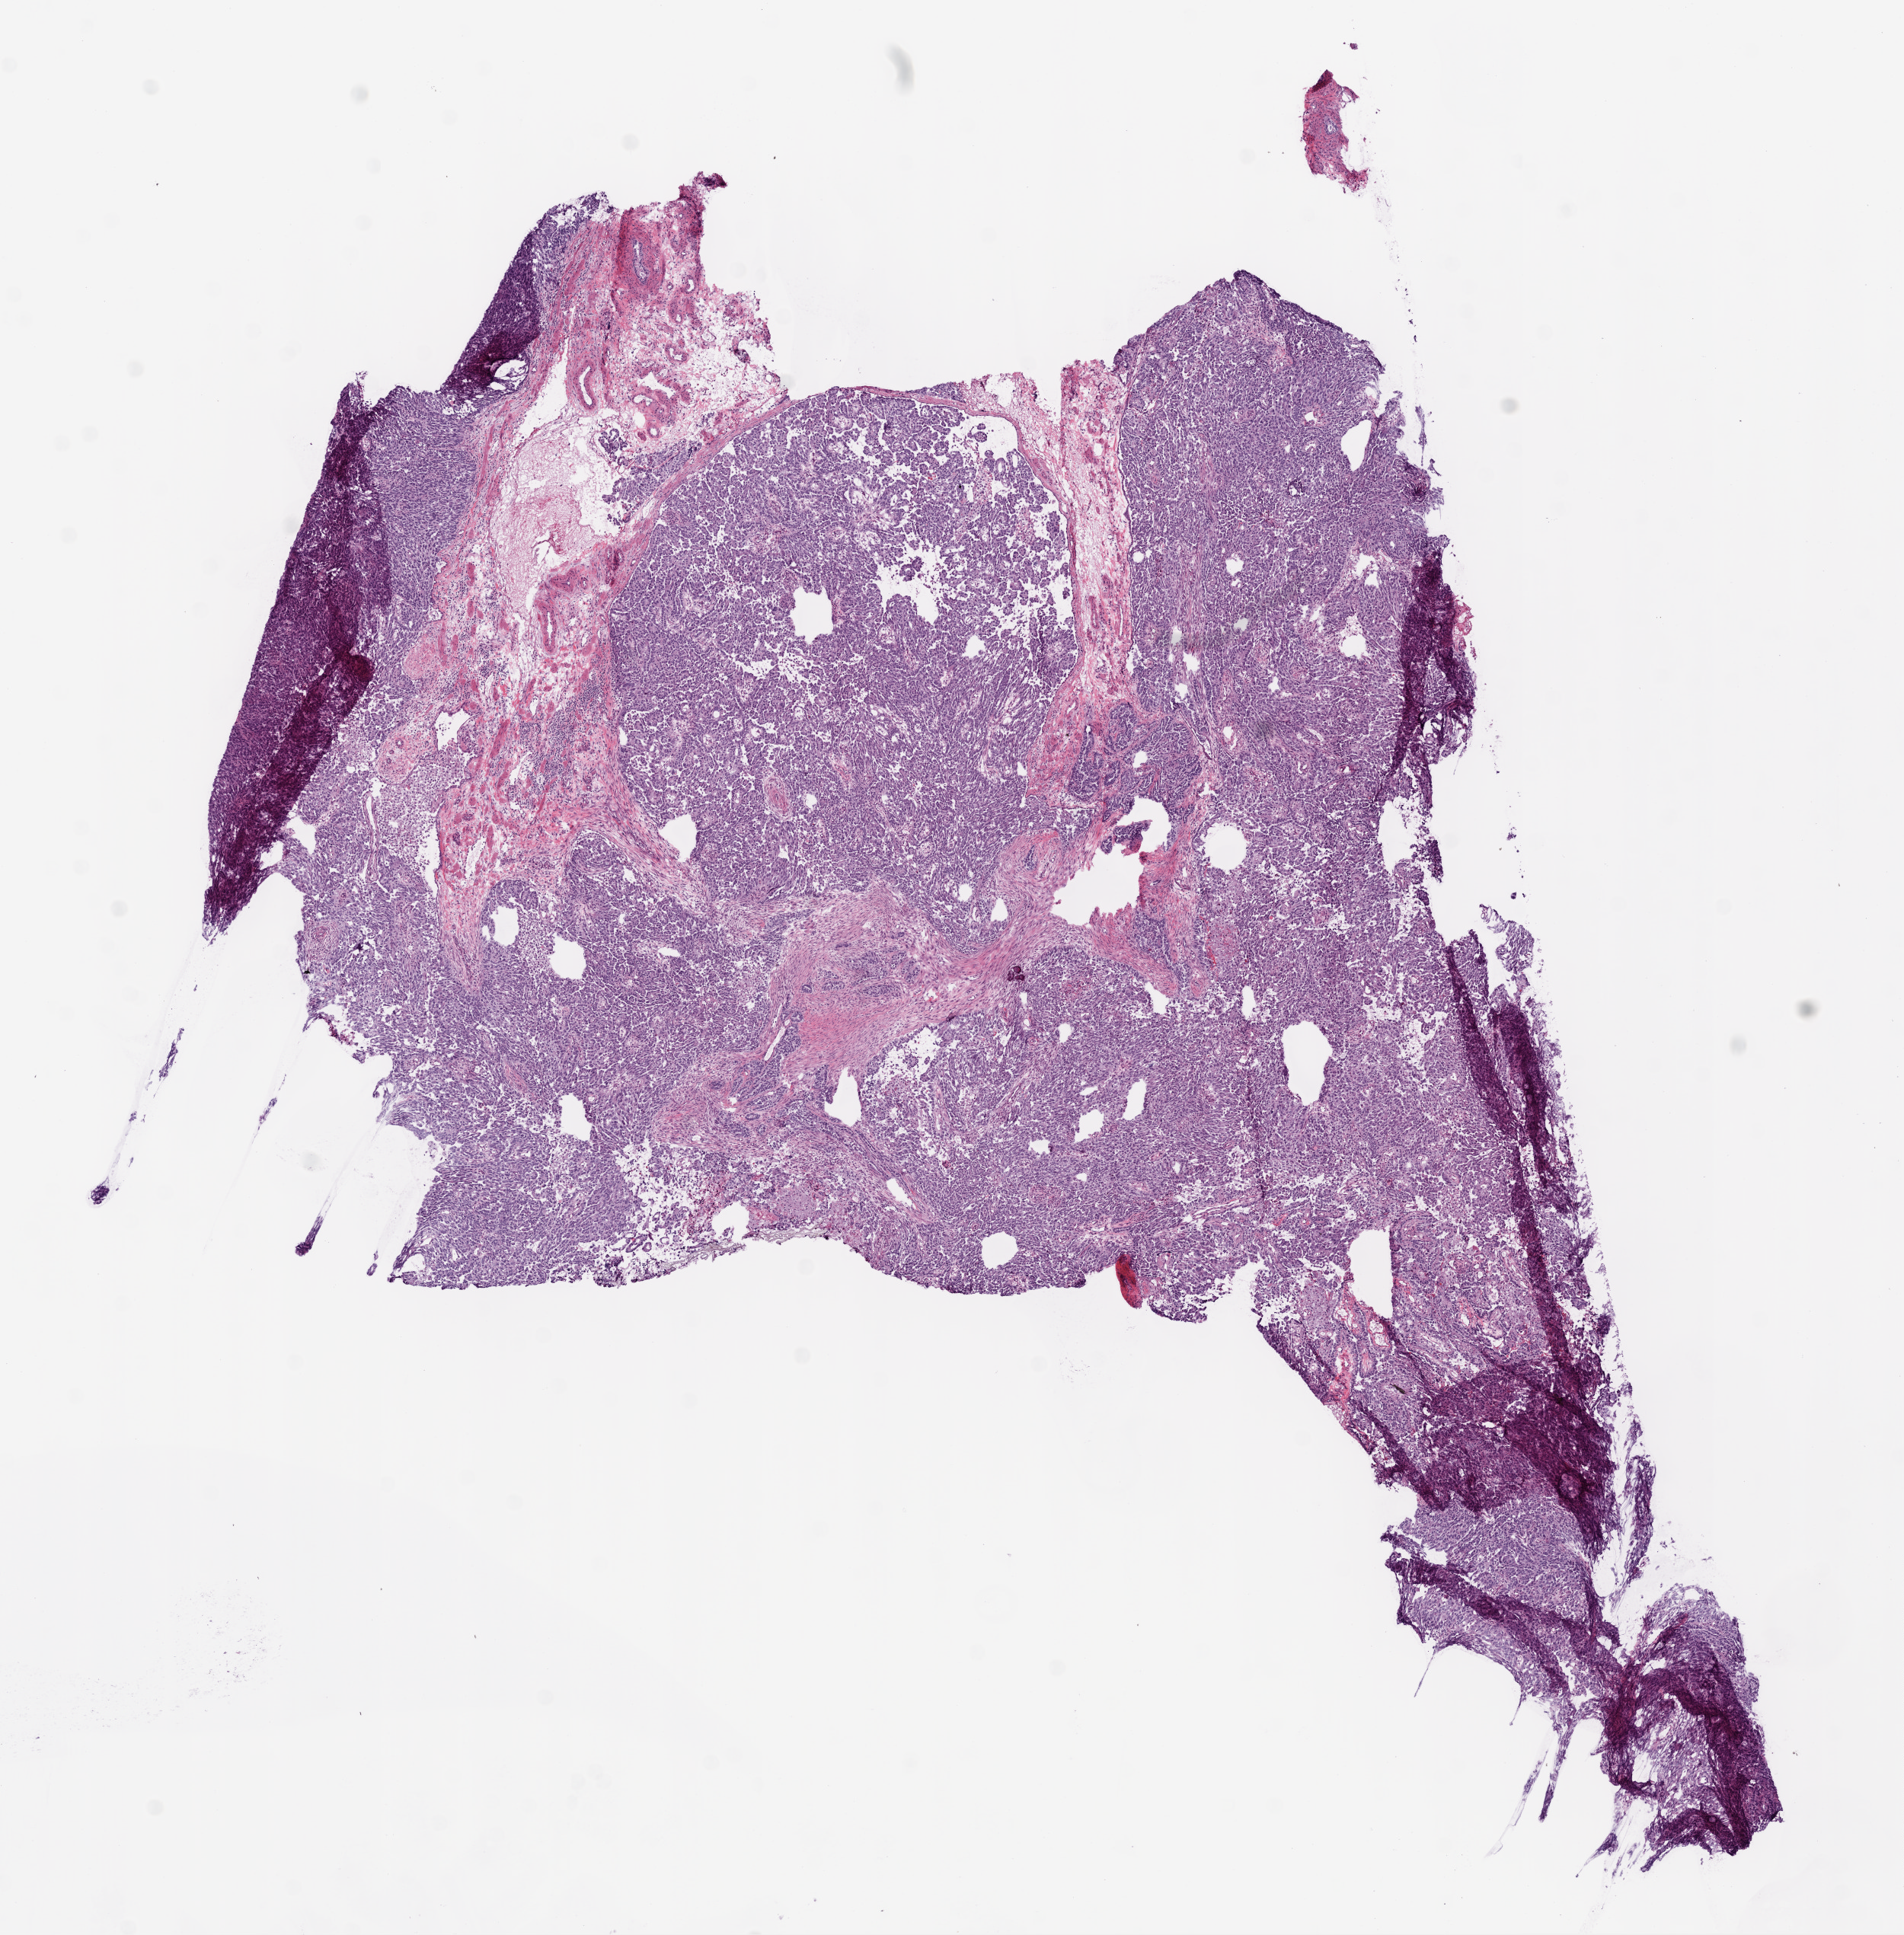
H&E-stained whole-slide image — whole scanned area (about 10.0 x 10.2 mm, slide scanned at 20x) shown as a low-resolution overview, frozen section from the bottom of the tissue portion, sample: primary tumour, ovary. Female patient; age at initial diagnosis 57 years. Composition of this section per pathologist review: tumour cells 85%, tumour nuclei 85%.
Histologic diagnosis: Serous cystadenocarcinoma, NOS.